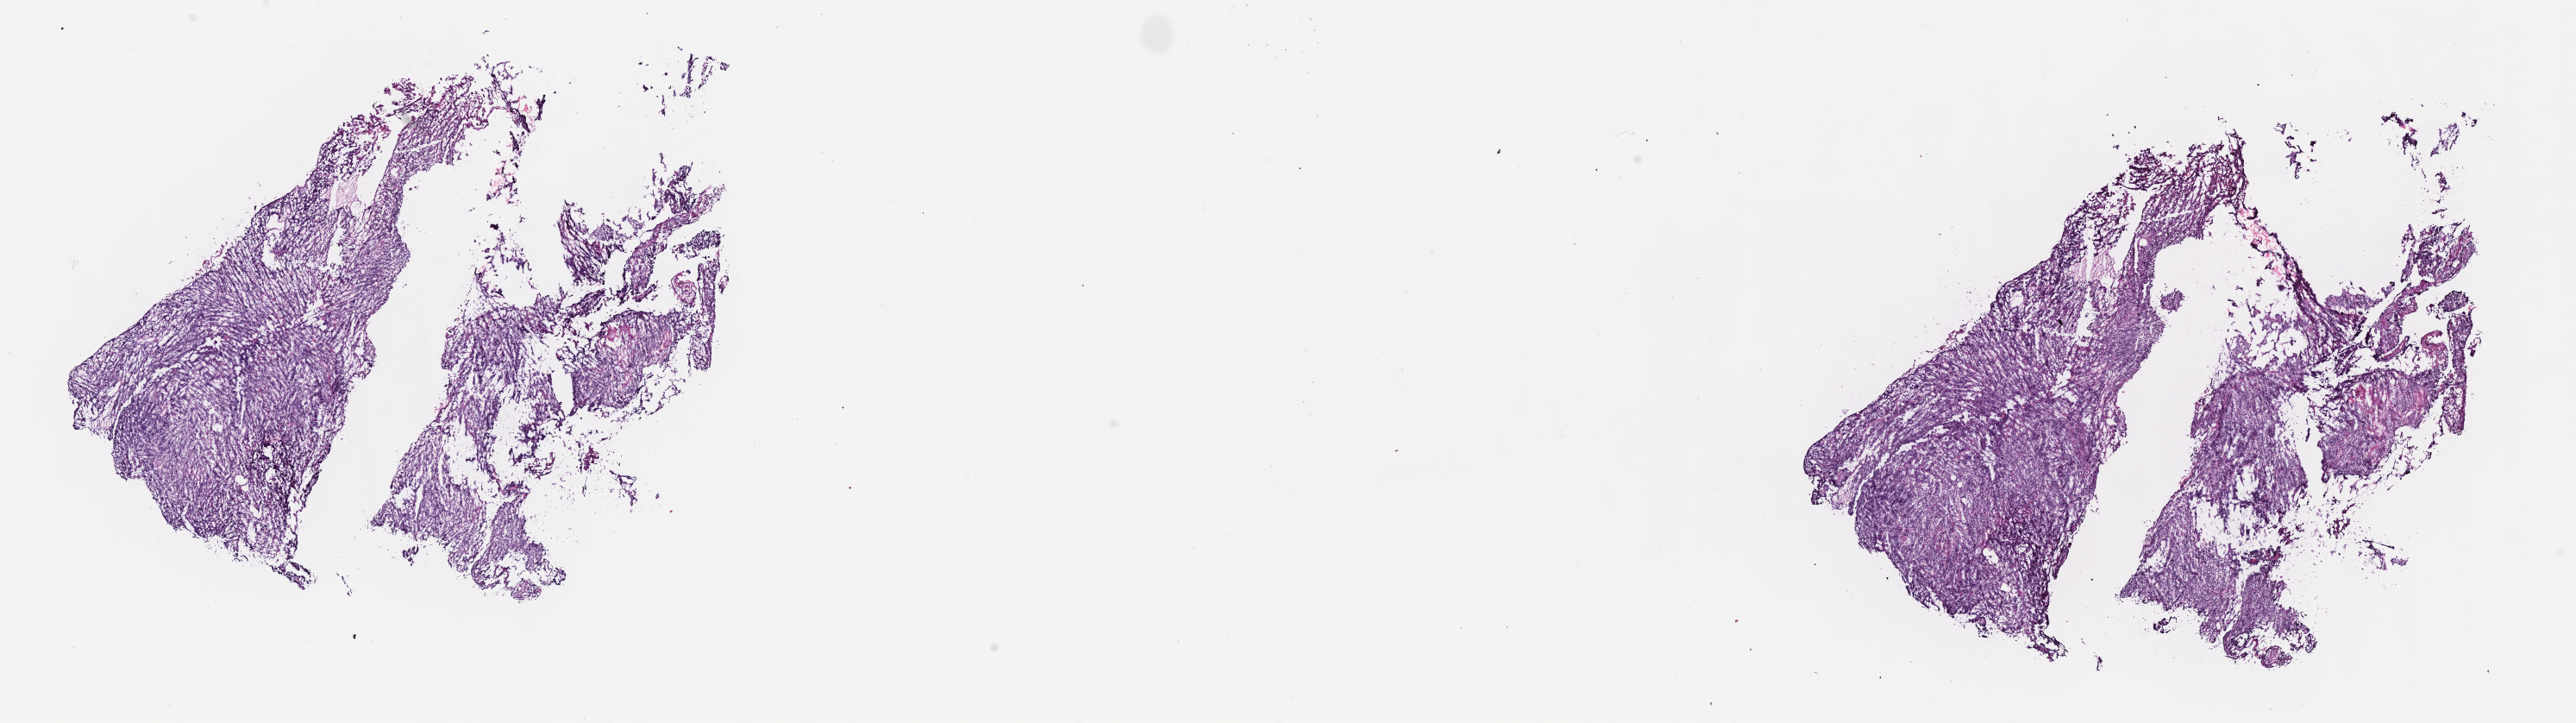
H&E whole-slide image — low-resolution overview of the scanned area, about 24.2 x 6.8 mm, cryosection, primary tumor, site: abdominal lymph node. Male, age 9 years at initial diagnosis. Slide review estimates, as recorded: tumor cells 90%, tumor nuclei 95%, stromal cells 5%, necrosis 5%, normal cells 0%. Infiltration values recorded for this section: lymphocyte infiltration 2%, monocyte infiltration 2%, neutrophil infiltration 0%.
Ann Arbor stage (patient): Stage III. Diagnosis: Burkitt lymphoma, NOS.